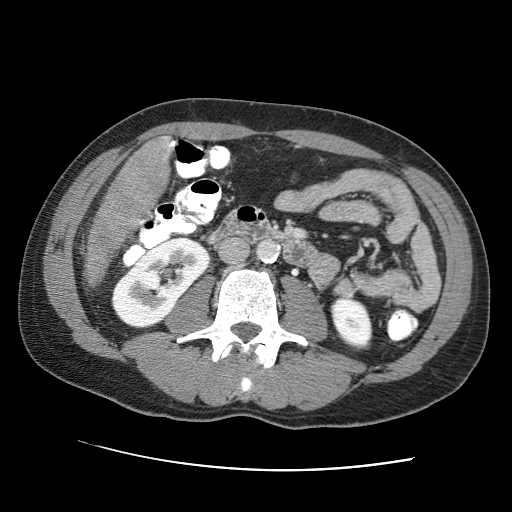
Contrast-enhanced abdominal CT (liver protocol), one axial slice. Slice 12 of 95 in the series (ordered by position). Reconstruction kernel STANDARD. One of 2 acquisitions stored at this slice position. Soft-tissue window (W 400 / L 40 HU). 2.5 mm slice thickness. 512 × 512 image matrix. Case-level facts recorded for this patient, not image findings: diagnosis: hepatocellular carcinoma (patient treated with transarterial chemoembolisation; whether this scan precedes or follows treatment is not stated here); TNM stage (as recorded): Stage-IVA; Child-Pugh class: A; tumour differentiation: moderately differentiated.
Outlined on this slice (semi-automatic segmentation, software-assisted and operator-edited):
- liver parenchyma outside the tumour (the mass and vessels are separate outlines, so this box may not span the whole liver): box from (x=139, y=136) to (x=174, y=225) px
- mass: (x=82, y=136)–(x=169, y=288)
- liver vessels: (x=168, y=142)–(x=174, y=150)